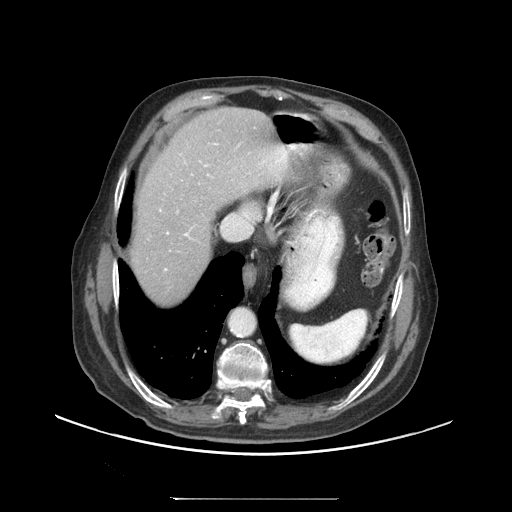
Contrast-enhanced abdominal CT (liver protocol), one axial slice. Position 82 of 97 along the scan axis. Reconstruction kernel STANDARD. 140 kVp. Soft-tissue window (W 400 / L 40 HU). 2.5 mm slice thickness. 512 × 512 image matrix, field of view 450 × 450 mm. Case-level facts recorded for this patient, not image findings: diagnosis: hepatocellular carcinoma (patient treated with transarterial chemoembolisation; whether this scan precedes or follows treatment is not stated here); TNM stage (as recorded): Stage-IIIC; Child-Pugh class: A; tumour differentiation: well differentiated; tumour nodularity: uninodular.
Annotated regions visible in this slice (semi-automatic segmentation, software-assisted and operator-edited):
- abdominal aorta: bounding box <231,308,256,335> (left, top, right, bottom; pixels)
- liver parenchyma outside the tumour (the mass and vessels are separate outlines, so this box may not span the whole liver): <130,108,290,304>
- liver vessels: <160,143,288,270>